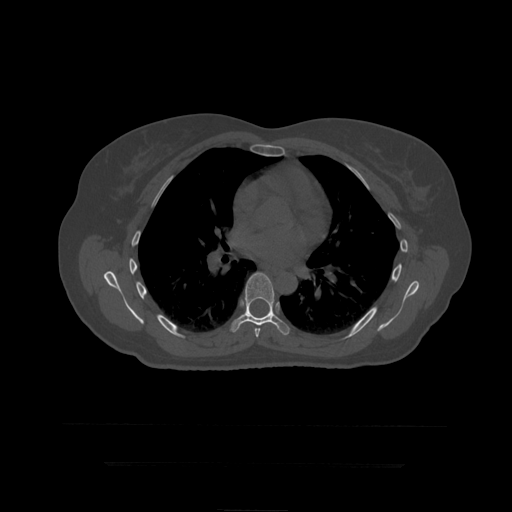
CT including the spine, one axial slice; position 286 of 399 along the scan axis; reconstruction kernel STANDARD; 120 kVp; bone window (W 1800 / L 400 HU); 1.25 mm slice thickness; 512 × 512 image matrix, field of view 450 × 450 mm. Patient age 41 years. From the clinical record (not read from this slice): primary cancer: breast.
Outlined on this slice (semi-automatic segmentation, software-assisted and operator-edited):
- T7 vertebra: bounding box [x1, y1, x2, y2] px = [255, 328, 261, 338]
- T8 vertebra: [230, 273, 290, 336]